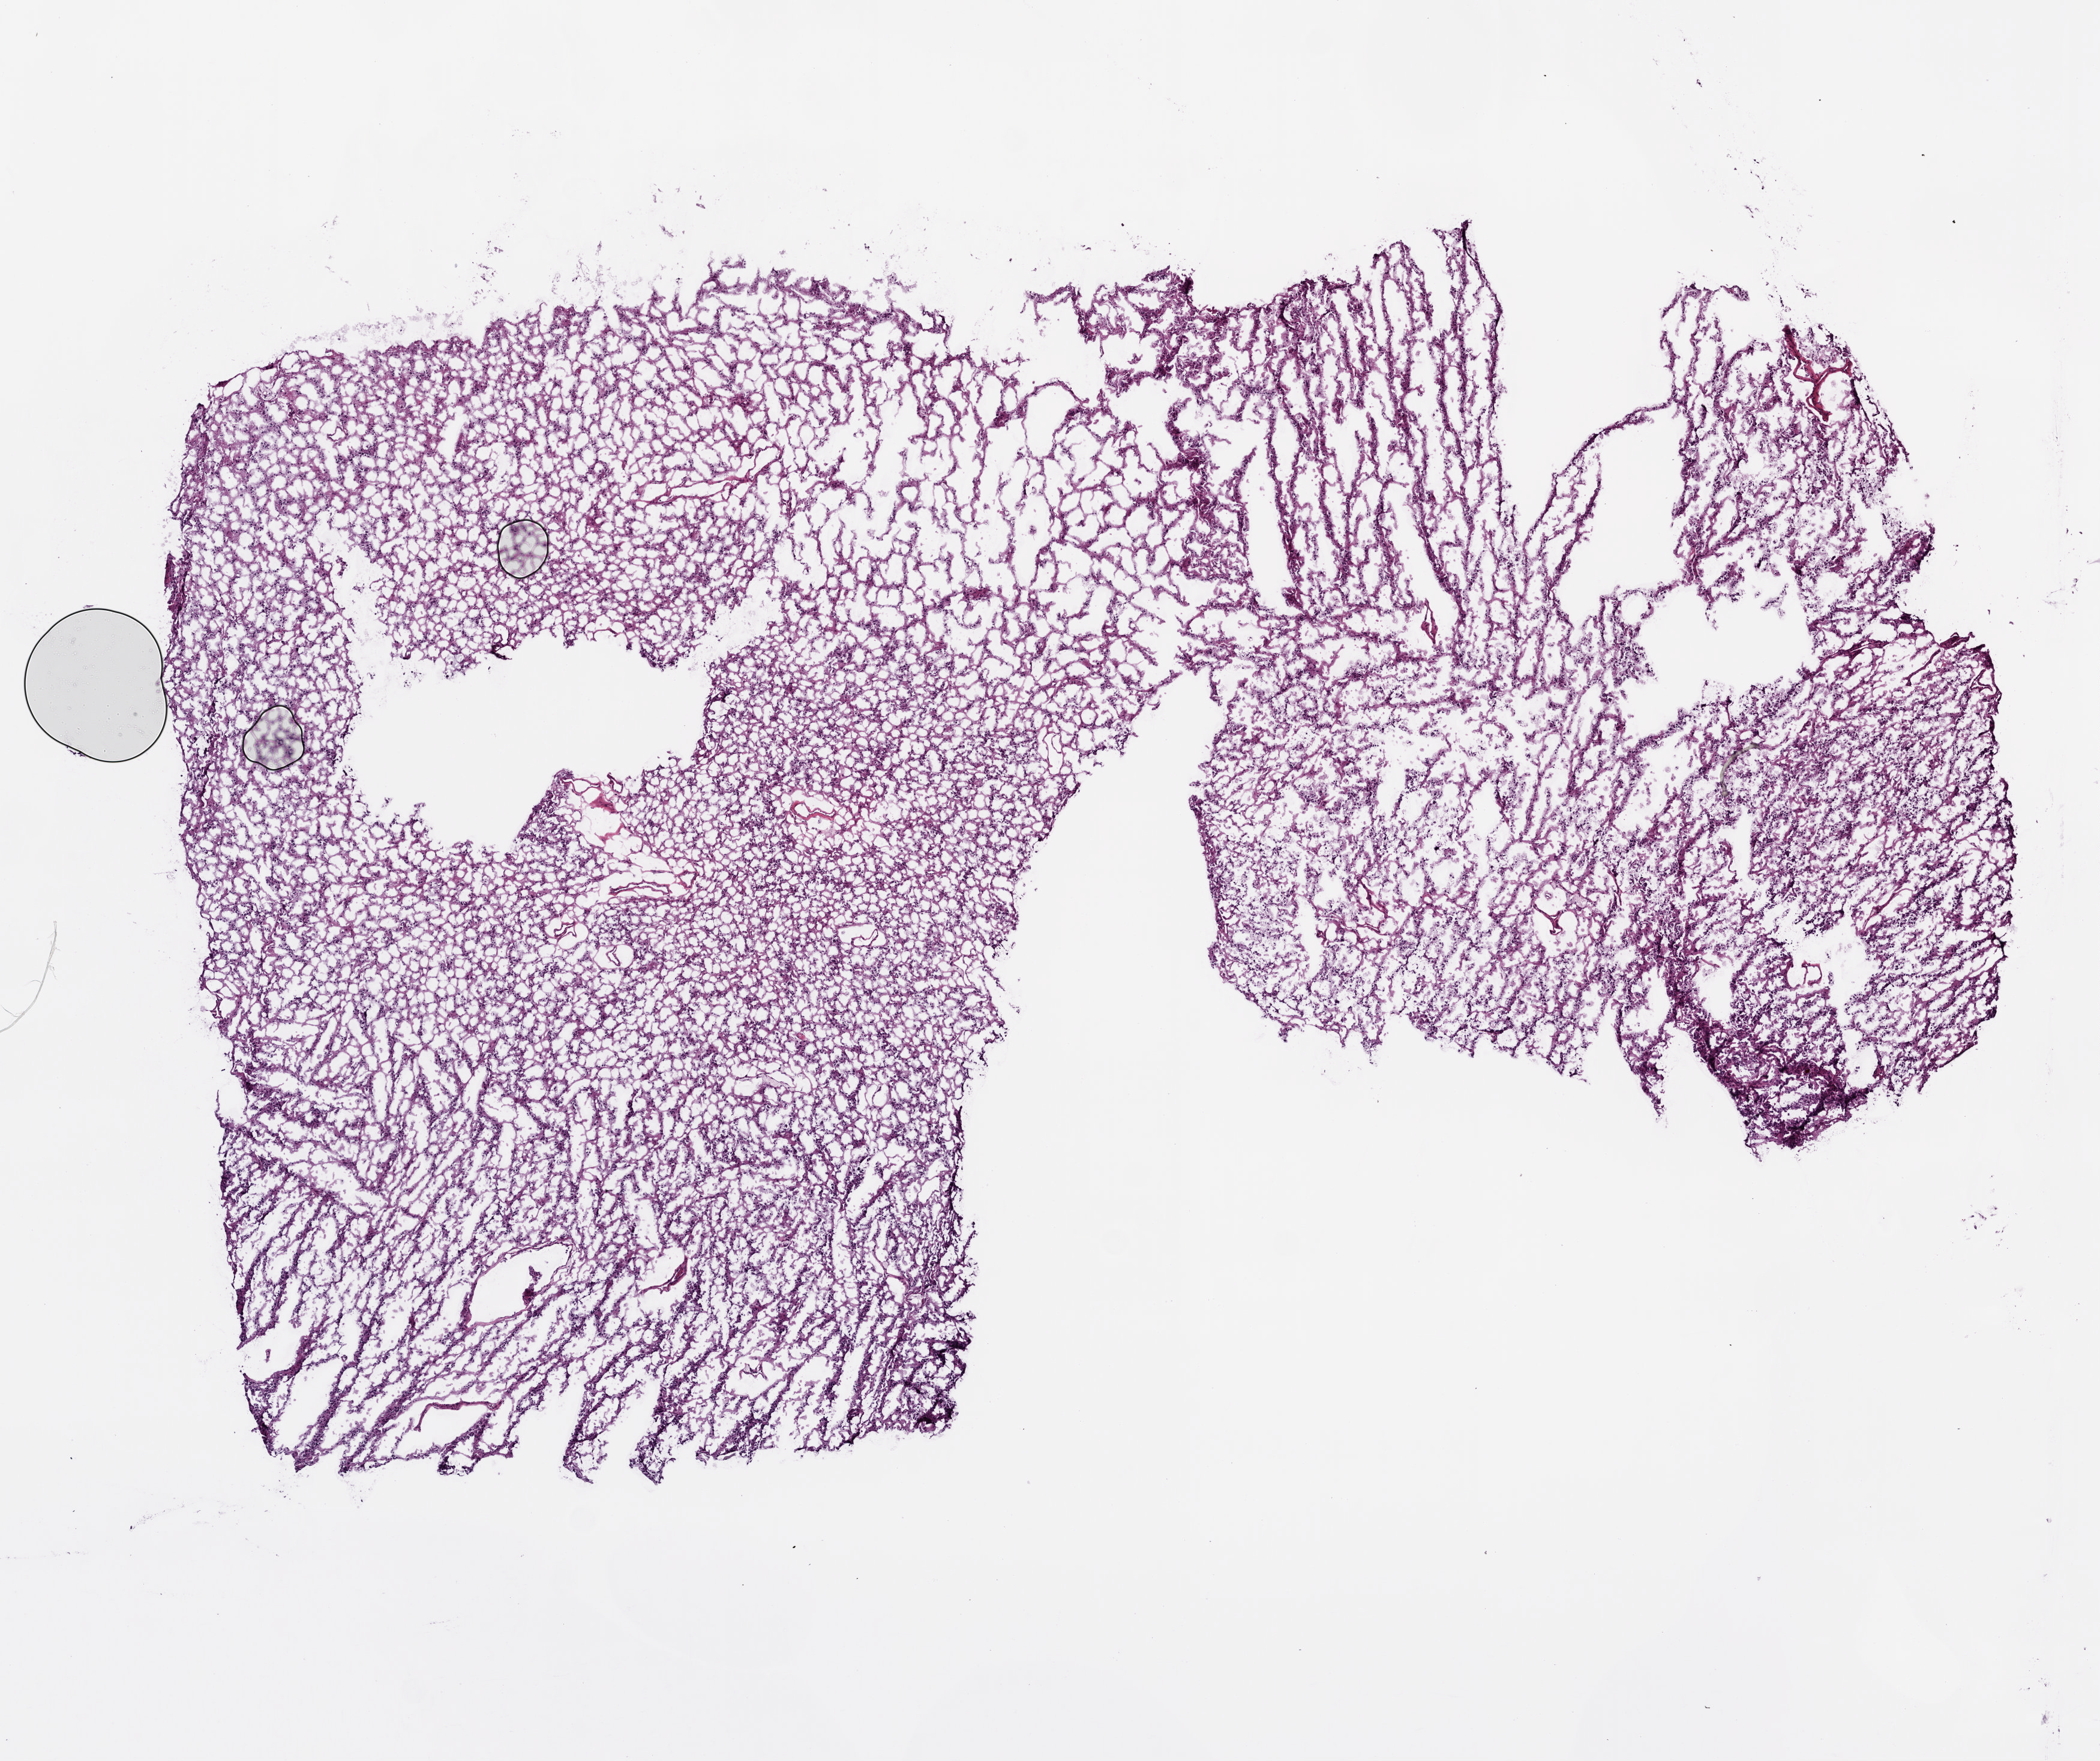
H&E-stained whole-slide image — low-resolution overview of the scanned area, about 7.0 x 5.9 mm (slide scanned at 20x). Frozen section. Sample: primary tumour, brain. Male, age 32 years at initial diagnosis. Histologic grade: G3 (poorly differentiated). Pathologist review of this section (percent, as recorded): tumour cells 100%, tumour nuclei 75%, normal cells 0%, stromal cells 0%, necrosis 0%.
• diagnosis: Oligodendroglioma, anaplastic (cerebrum)